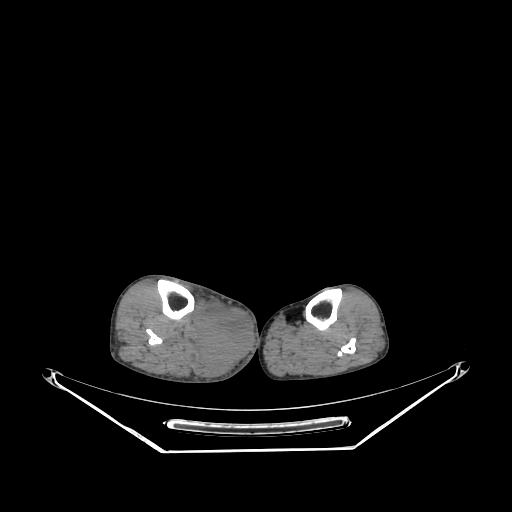
CT of an extremity soft-tissue mass (from a PET/CT study), one axial slice. Position 133 of 267 along the scan axis. Soft-tissue window (W 400 / L 40 HU). 512 × 512 image matrix. Male patient. Case-level facts recorded for this patient, not image findings: histological type: pleiomorphic liposarcoma; grade: high; site of the primary tumour: right calf.
Outlined on this slice (expert contour drawn on MRI and transferred to this co-registered scan by the dataset authors):
- gross tumour volume including surrounding oedema: bounding box (x1, y1, x2, y2) in pixels: (196, 299, 254, 378)
- gross tumour volume (mass): (198, 306, 254, 364)